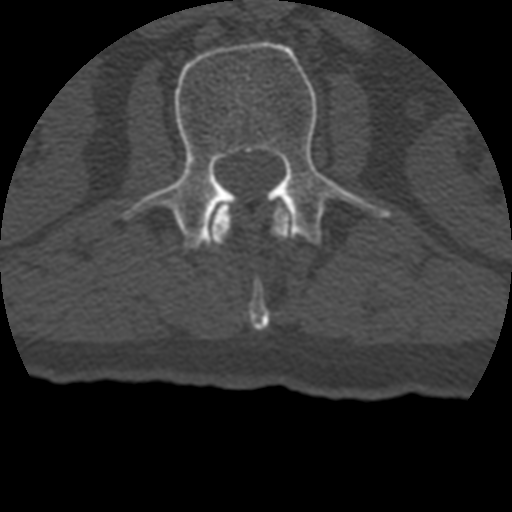
CT including the spine, one axial slice; reconstruction kernel STANDARD; bone window (W 1800 / L 400 HU); 1.25 mm slice thickness; 512 × 512 image matrix, field of view 160 × 160 mm. Patient age 69 years. From the clinical record (not read from this slice): primary cancer: prostate.
Structures marked on this image (semi-automatic segmentation, software-assisted and operator-edited):
- L1 vertebra: bounding box [x1, y1, x2, y2] px = [211, 201, 293, 330]
- L2 vertebra: [117, 41, 394, 250]